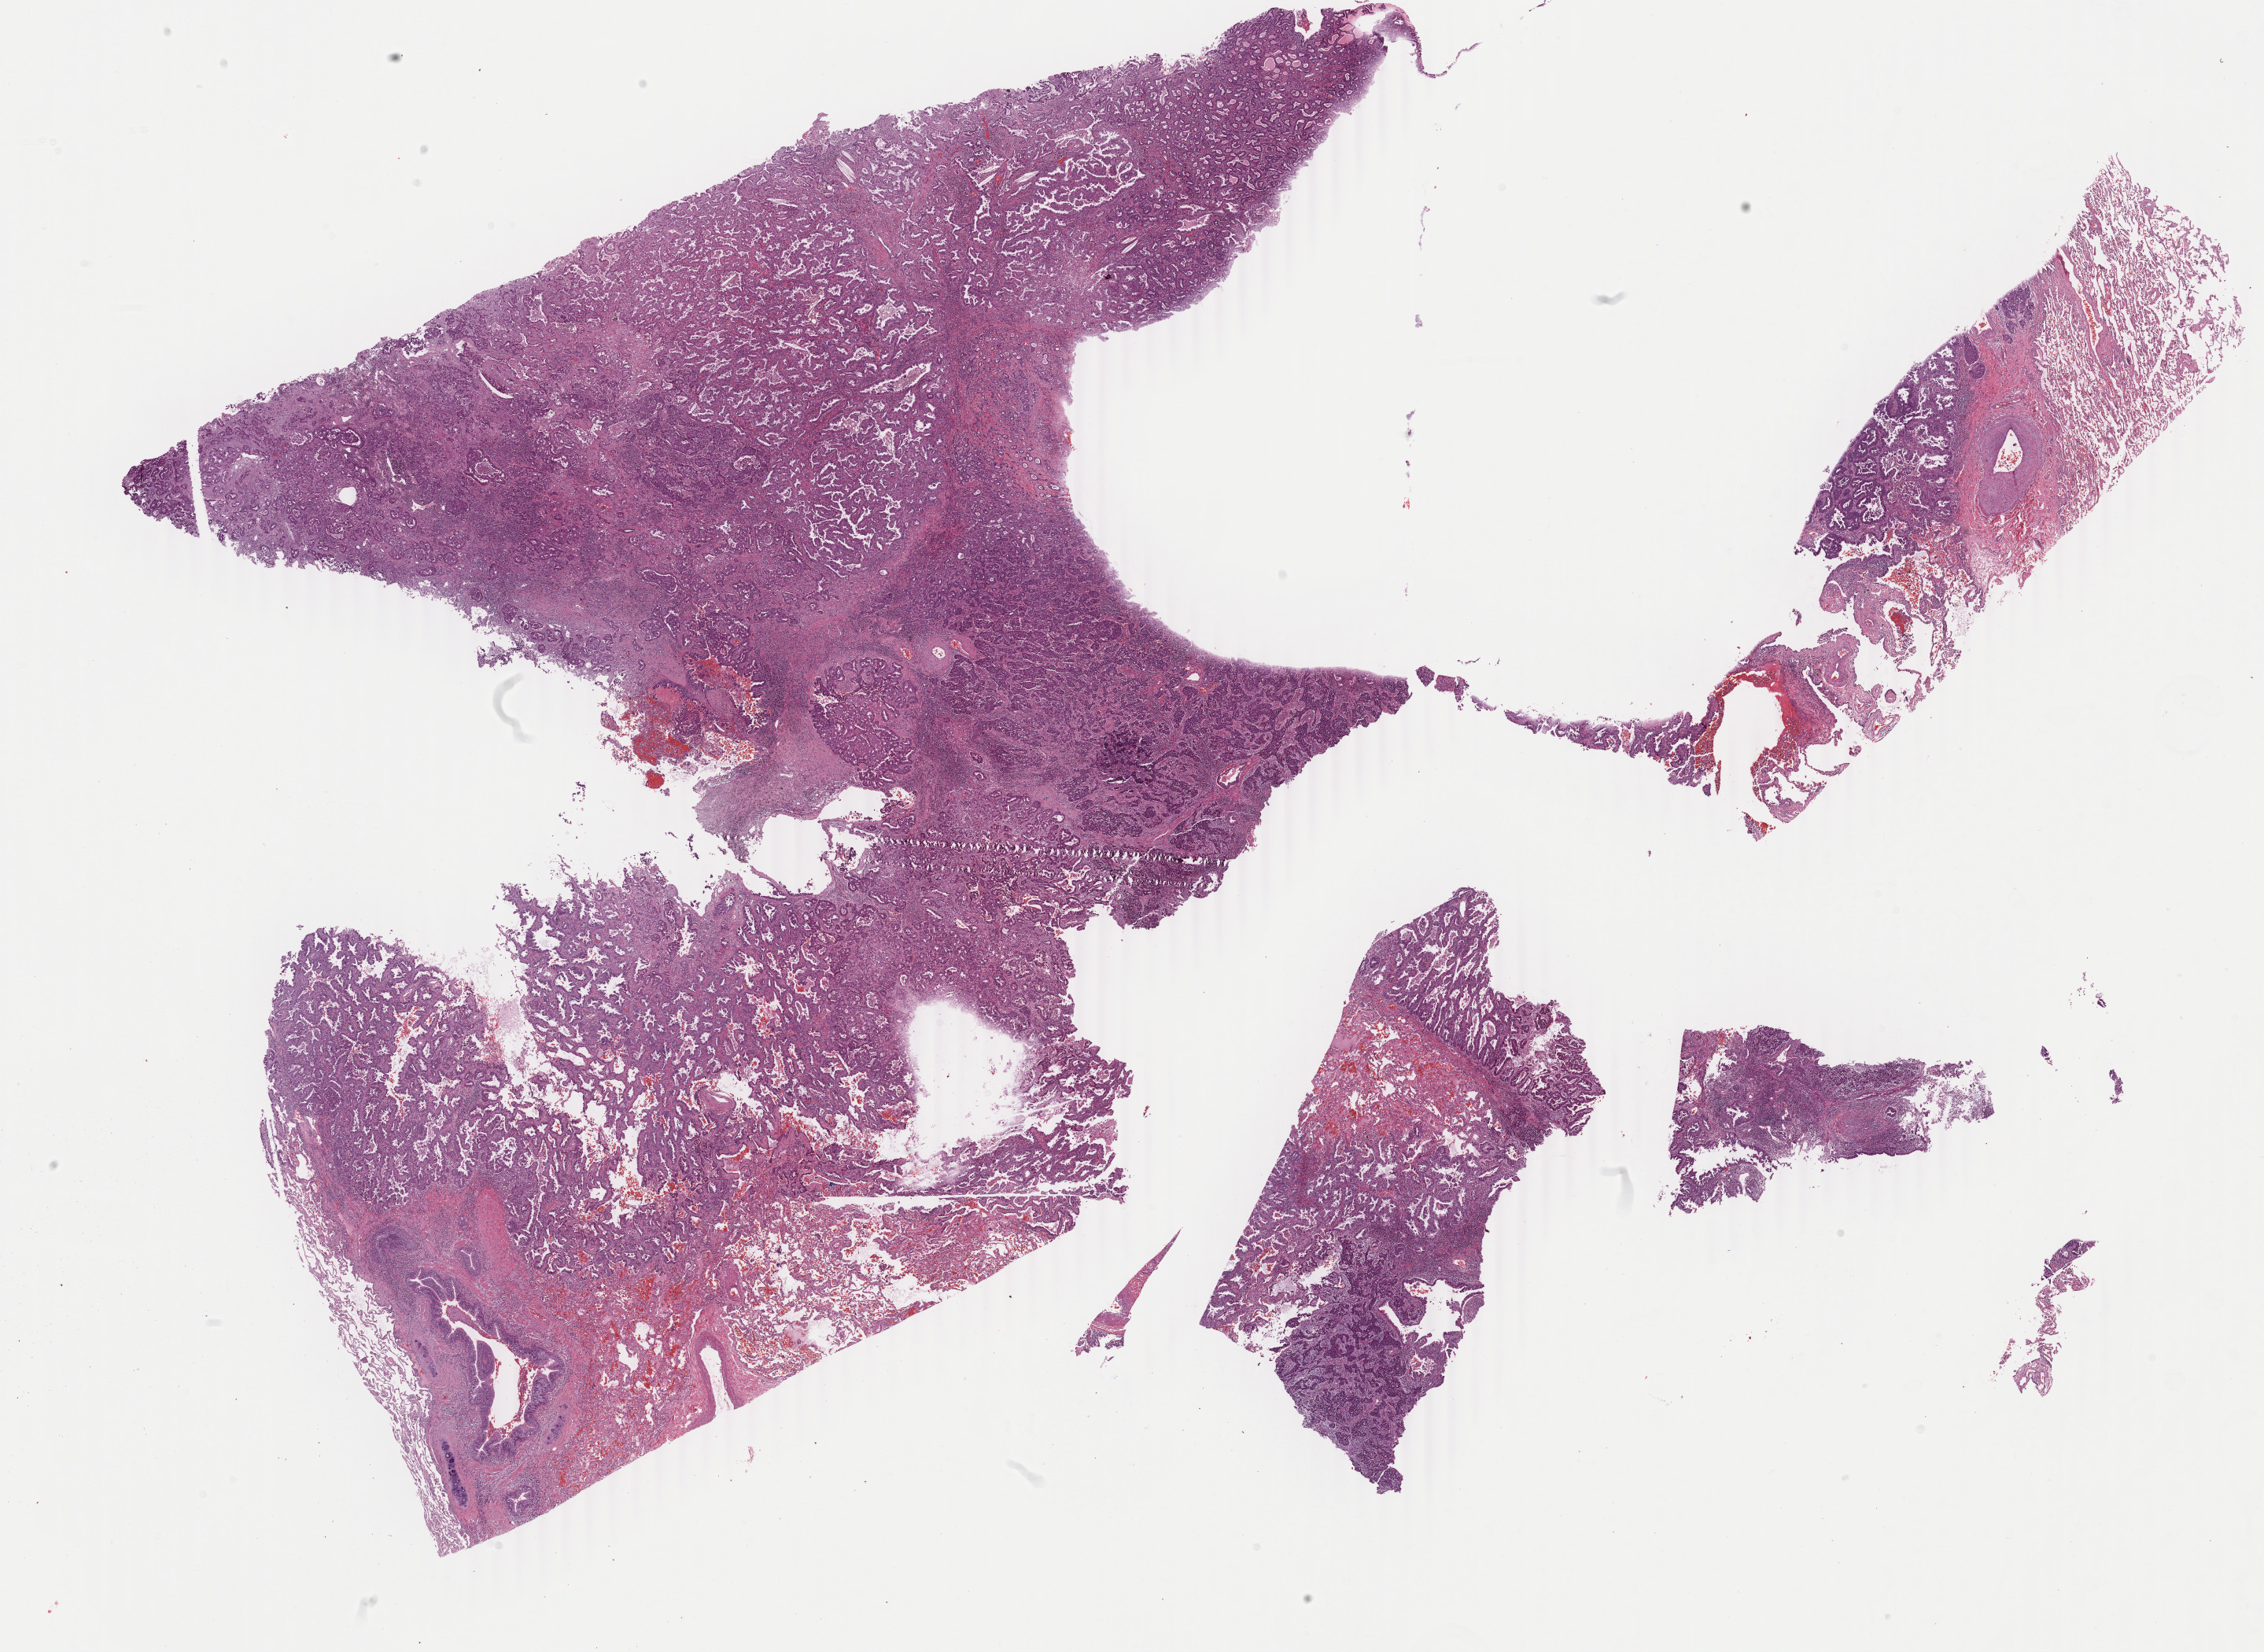
Whole-slide image, H&E stain, a low-resolution overview of the entire scanned area, about 22.9 x 16.7 mm. Specimen: tumor tissue. Anatomic site: lung (right). Male patient, 51 years old.
Histologic diagnosis: Adenocarcinoma, NOS.